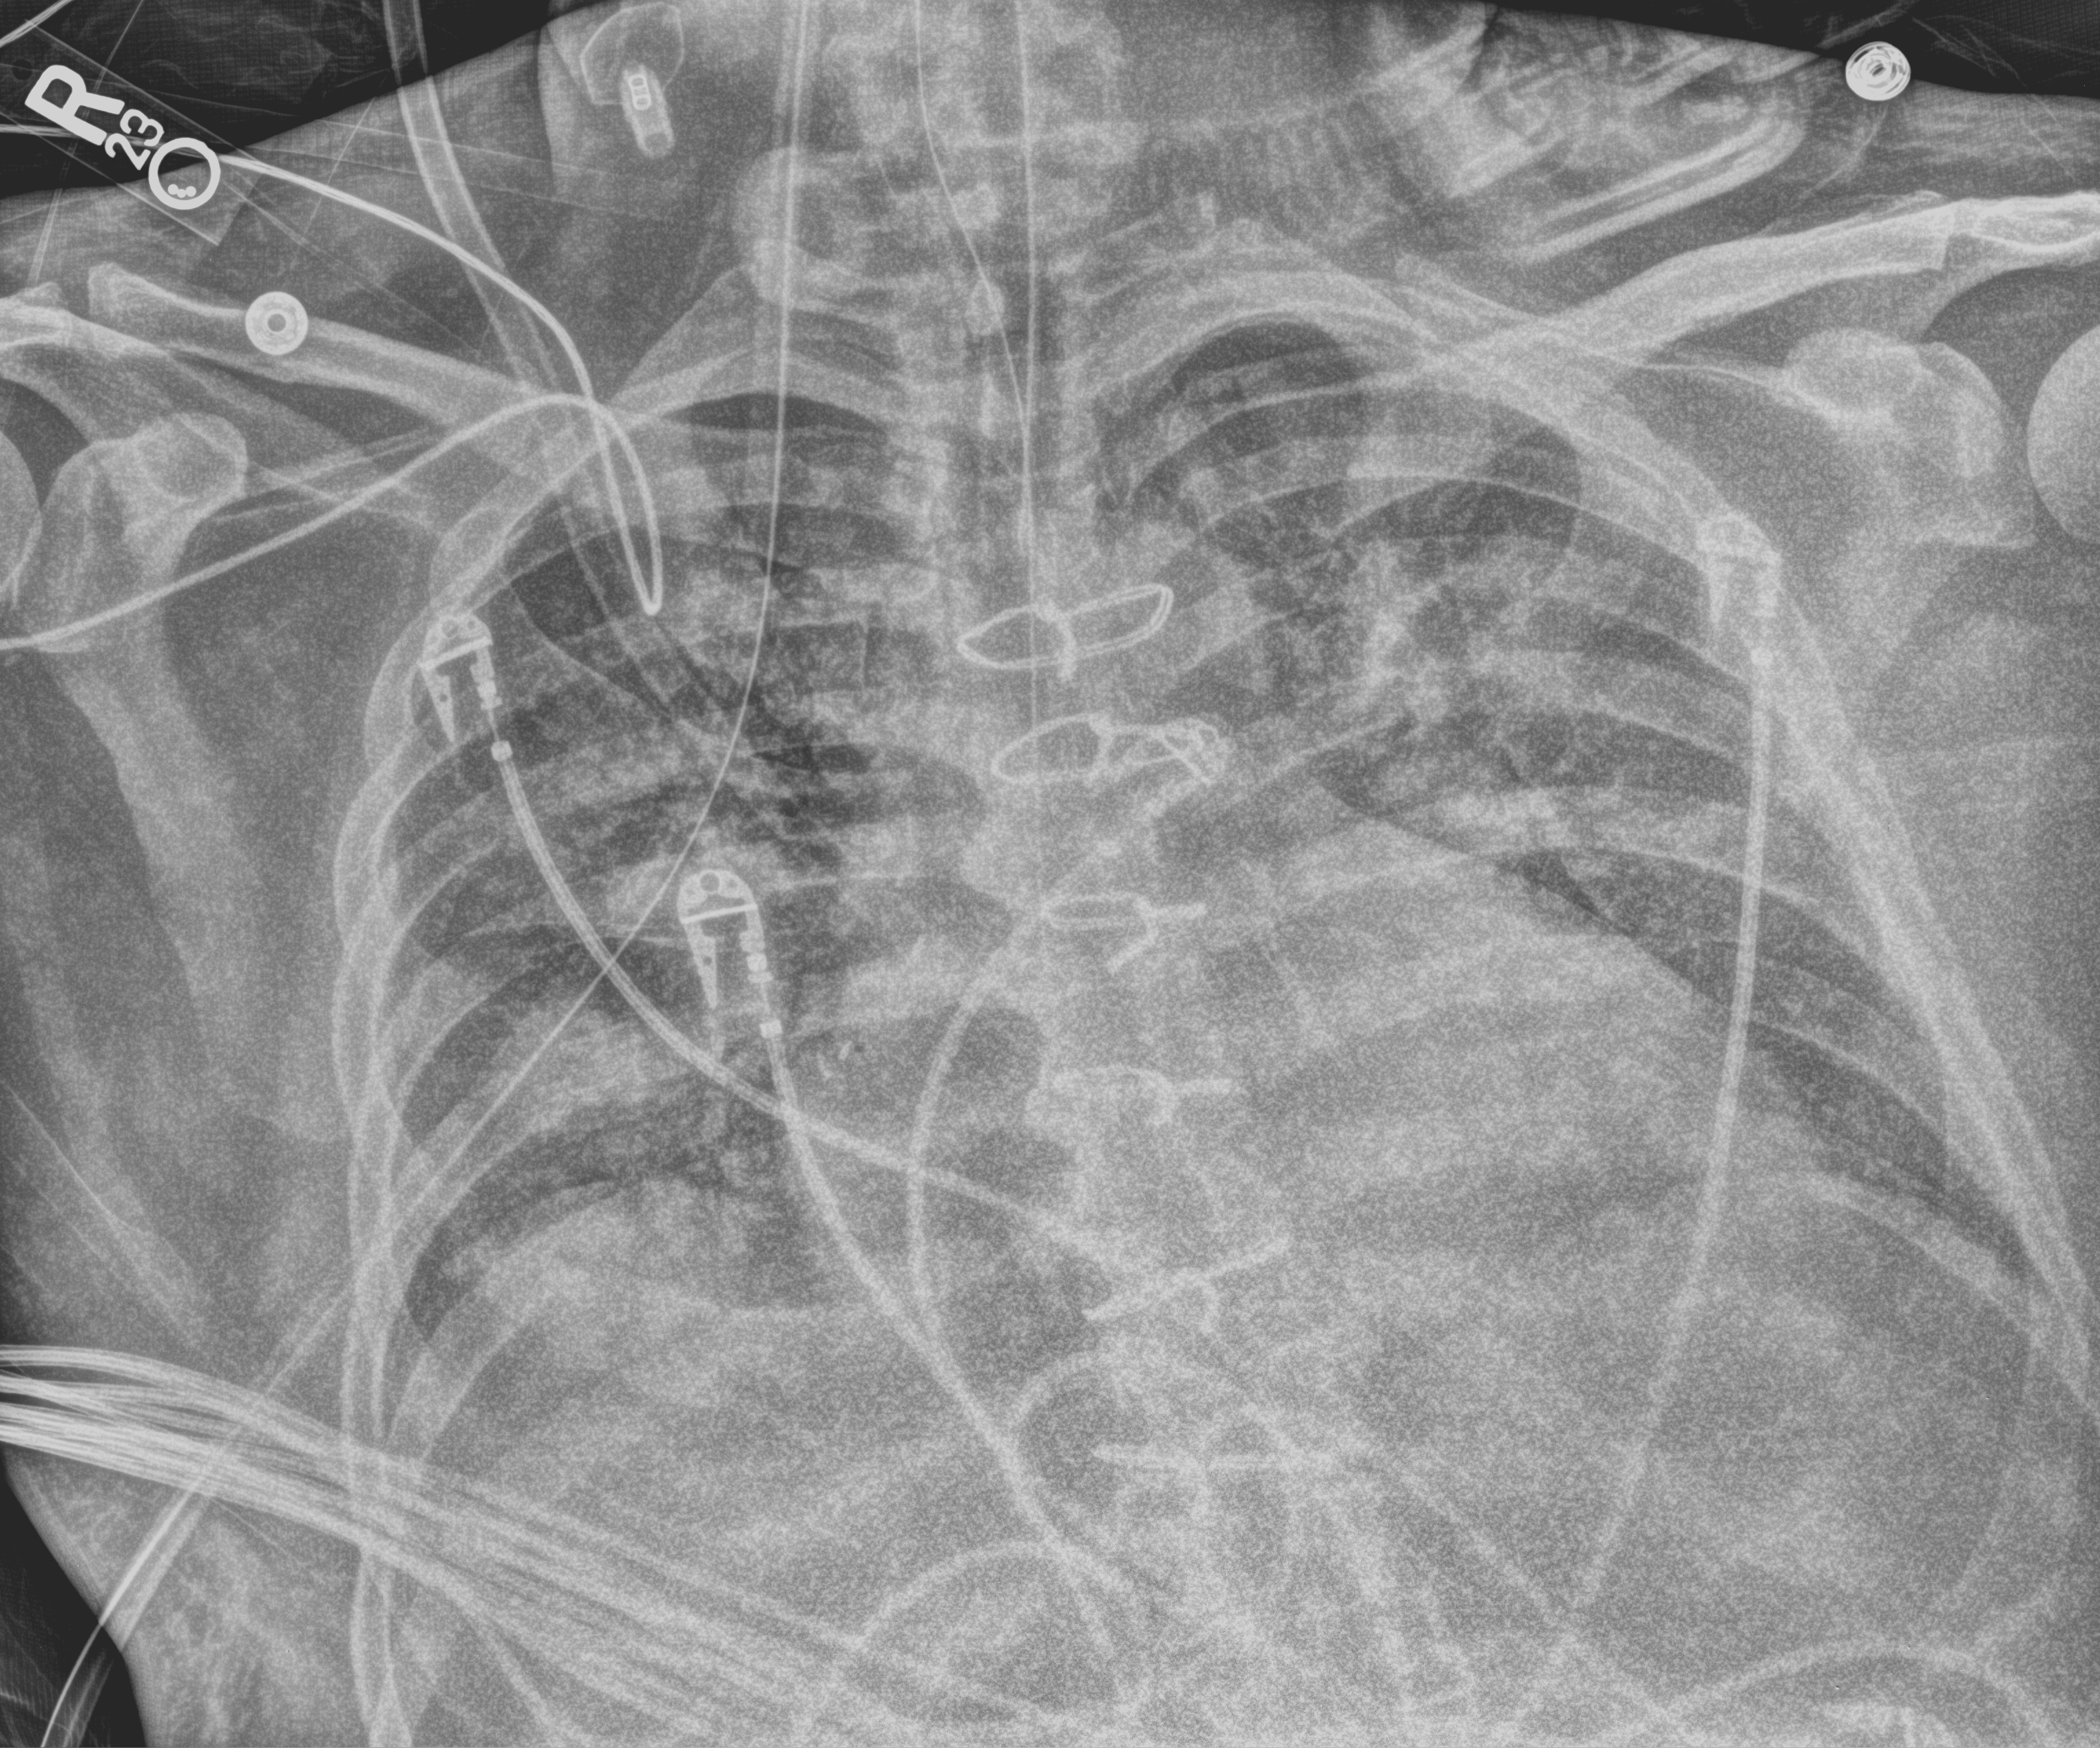
Portable chest radiograph; anteroposterior (AP) projection. Patient hospitalised with COVID-19, aged 18–59 years.
Hospital-stay facts (about this admission, not read from this image; timing relative to this image not recorded): diabetes (admission record): yes; mechanically ventilated during this hospital stay: yes.